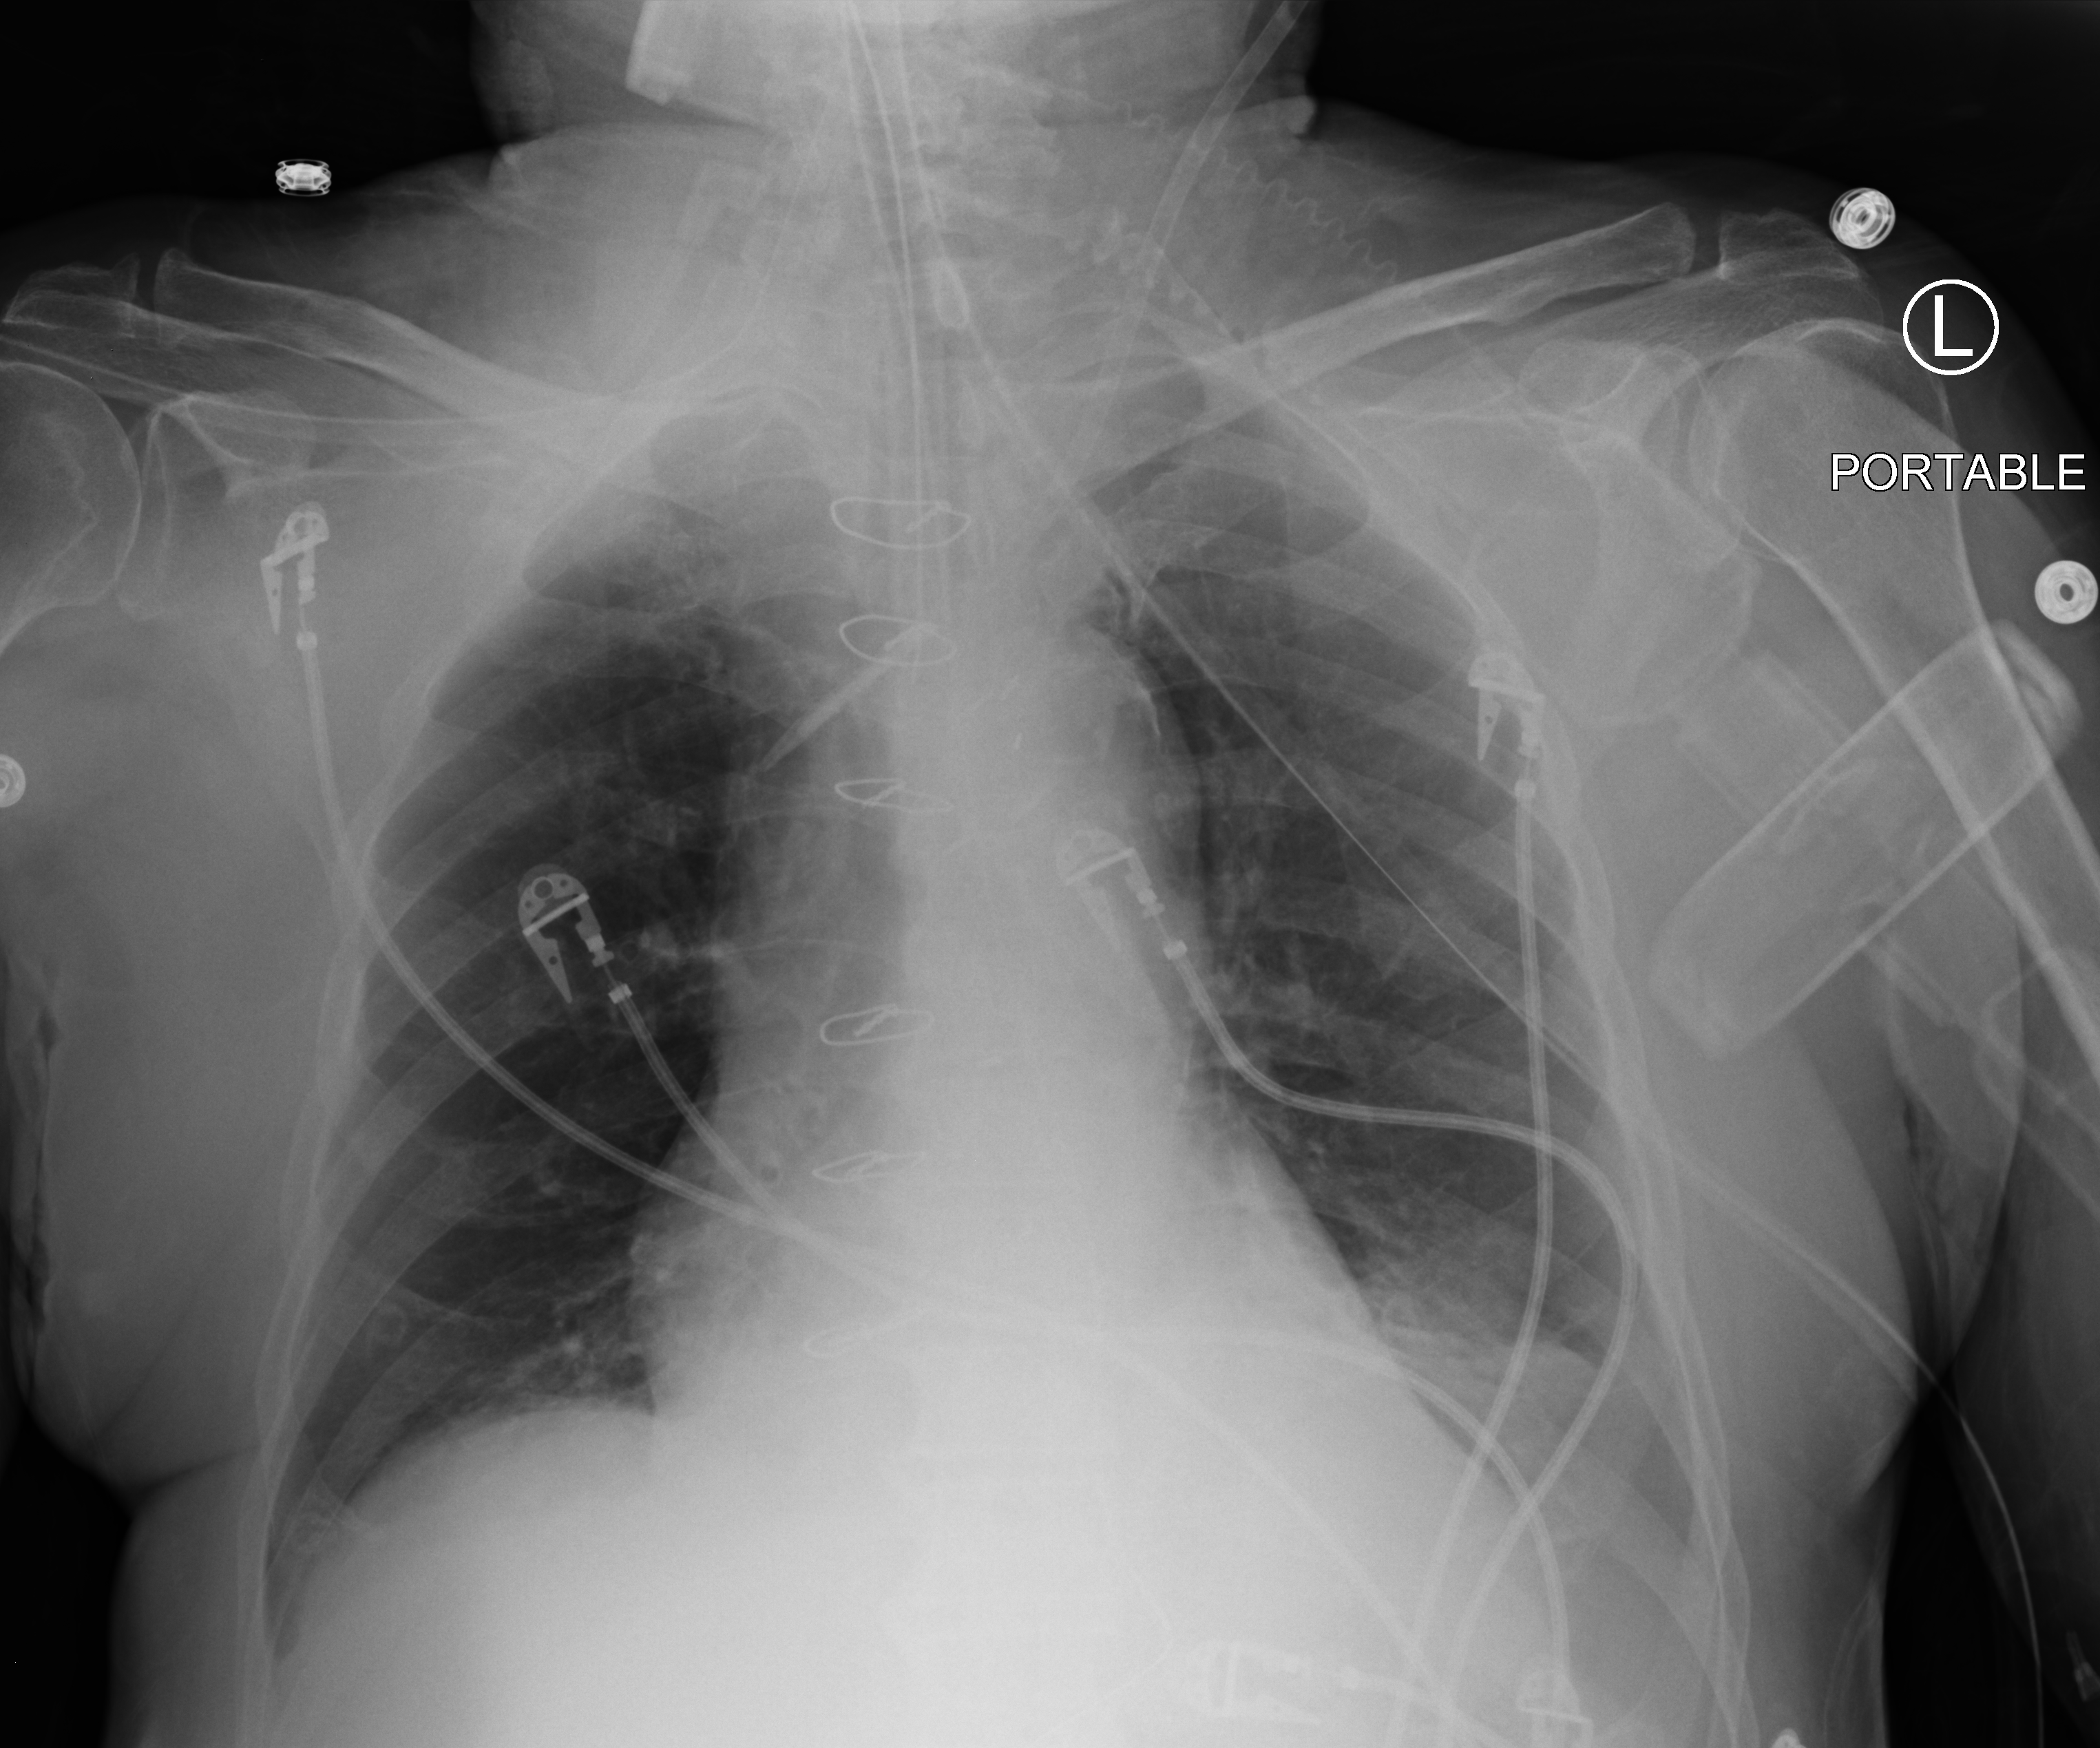
Chest X-ray (portable). Patient hospitalised with COVID-19; male, aged 75–90 years.
From the hospital-stay record, not from the radiograph (when in the stay this image was taken is not recorded): mechanically ventilated during this hospital stay: yes; other chronic lung disease (admission record): no.